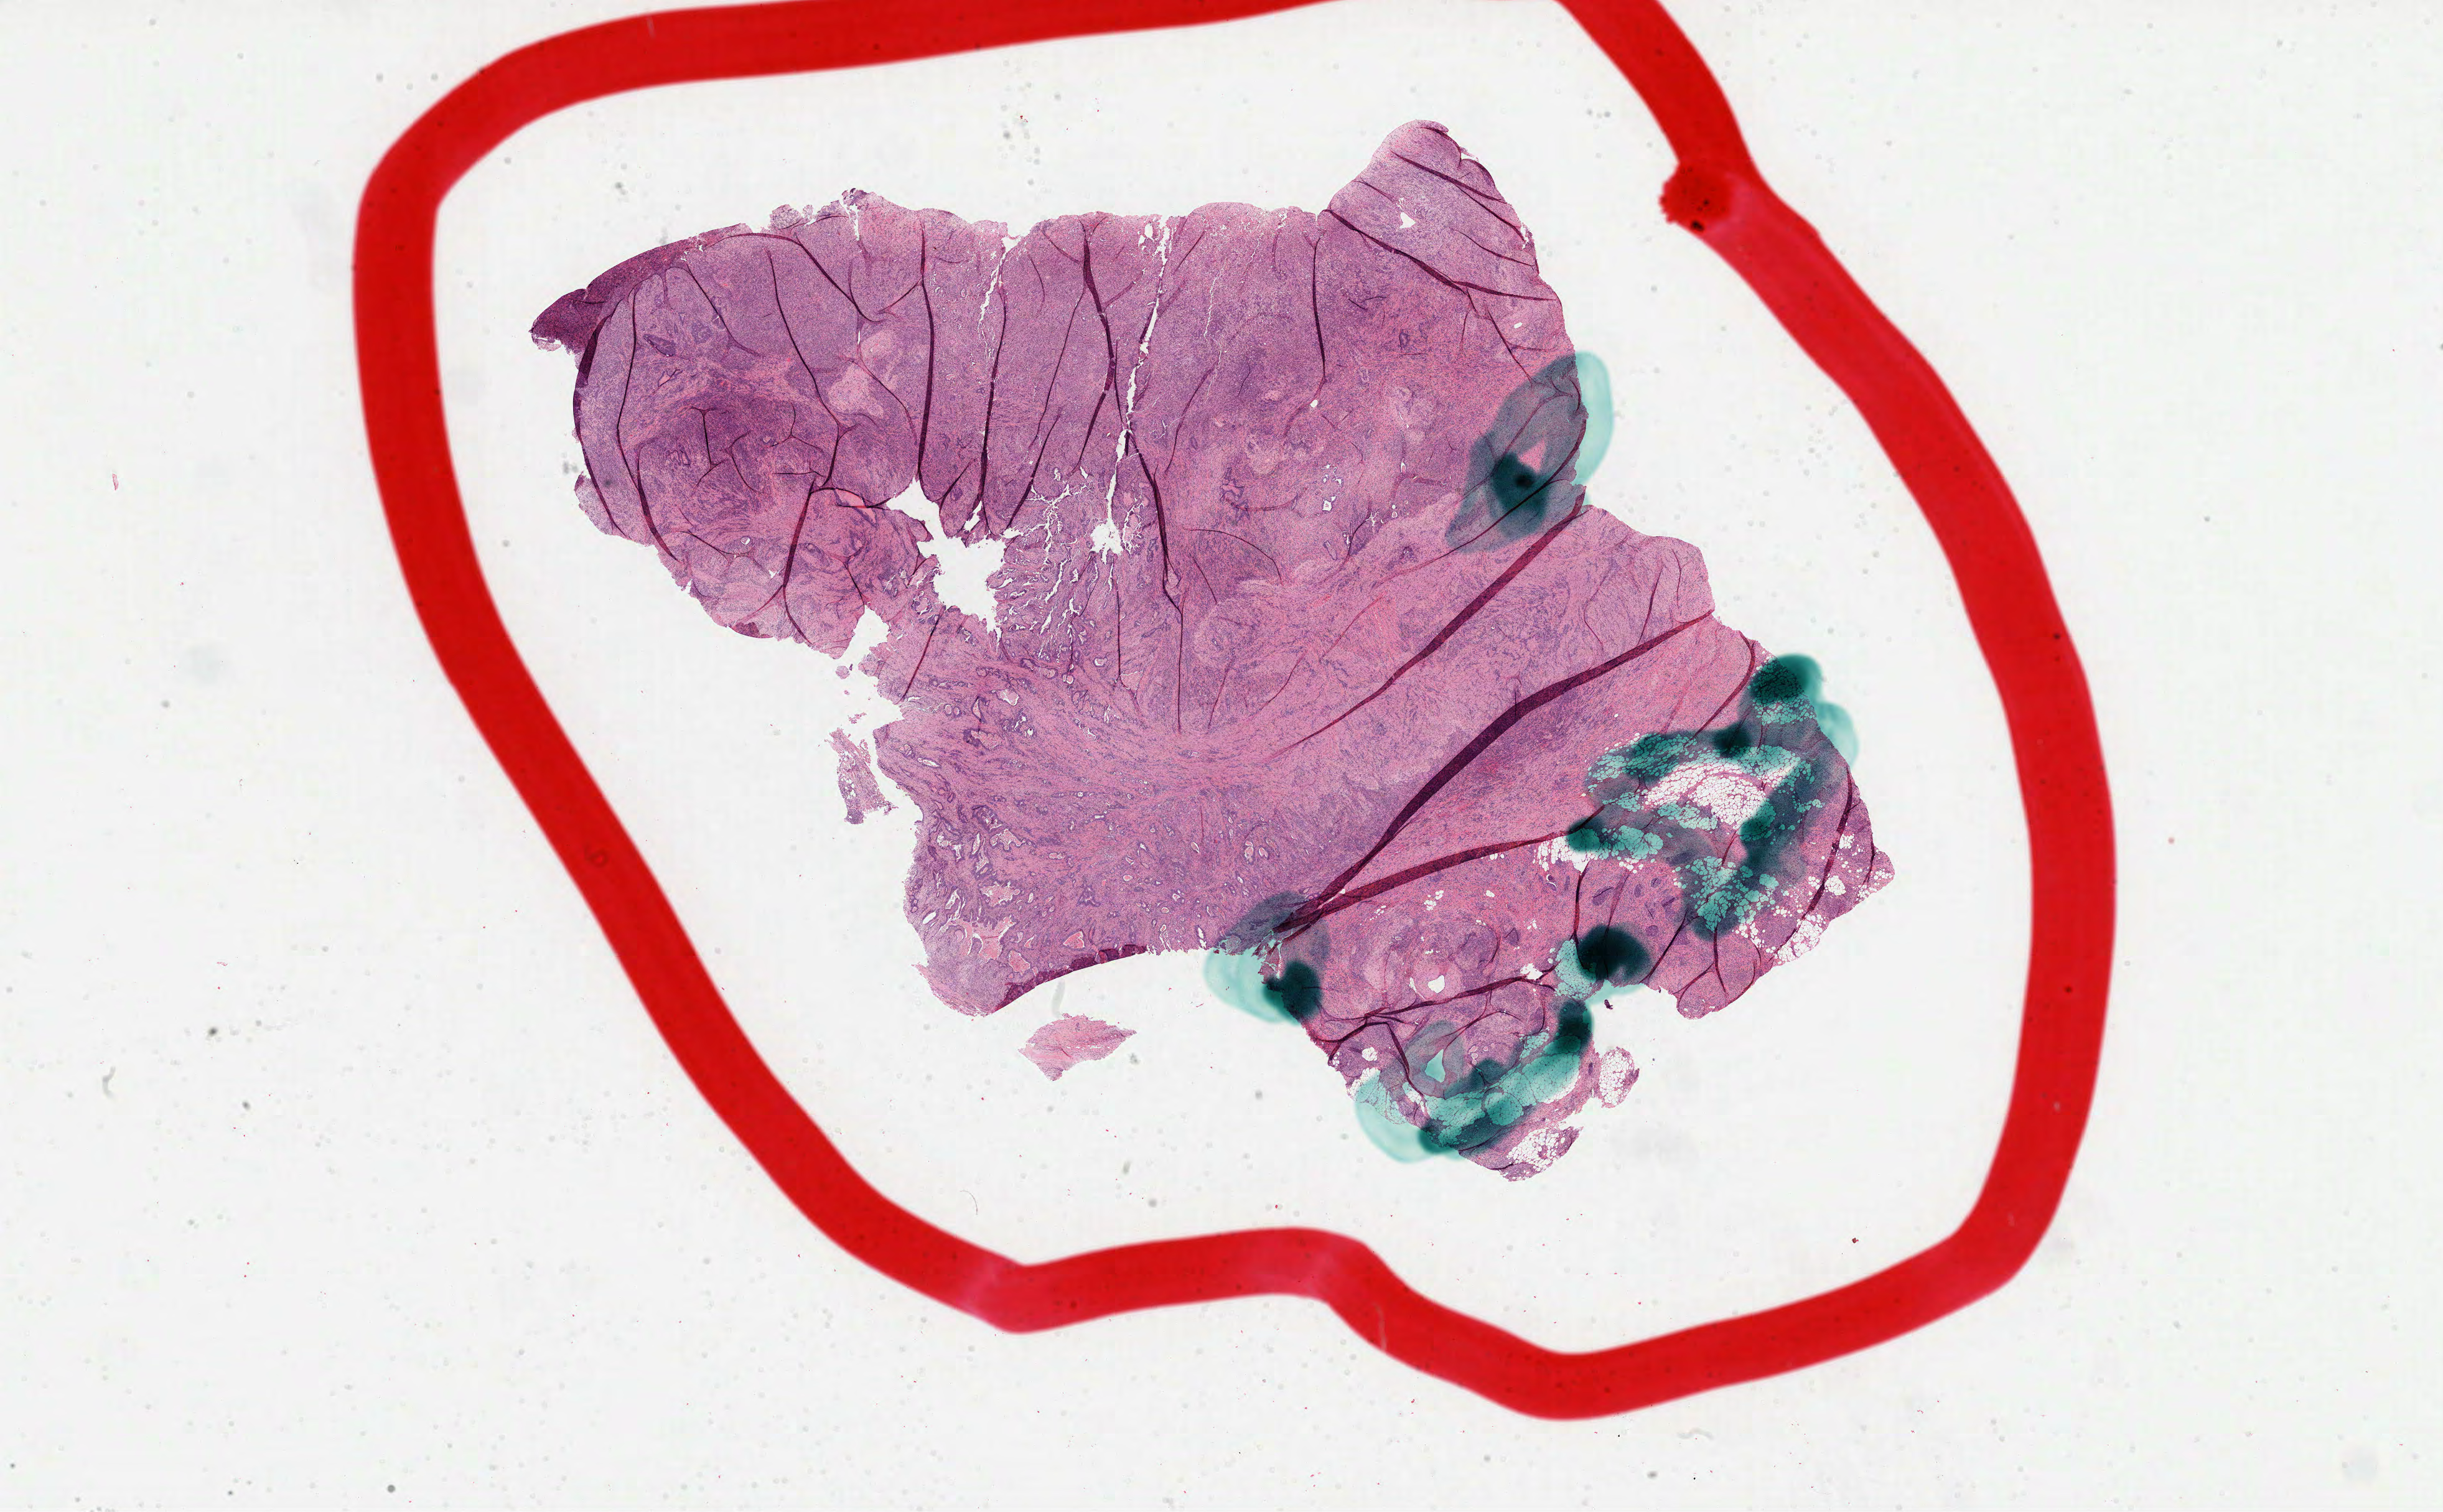
Digitized H&E-stained tissue section (whole slide), whole scanned area (about 31.7 x 19.6 mm, slide scanned at 40x) shown as a low-resolution overview. Formalin-fixed paraffin-embedded (FFPE) diagnostic section. Stomach, primary tumour sample. Patient: male, age at initial diagnosis 63 years. Histologic grade: G3 (poorly differentiated).
AJCC pathologic stage: IIIA (6th edition). Histologic diagnosis: Adenocarcinoma, NOS (cardia, NOS). Lymph nodes positive (case pathology): 5 of 15 examined.